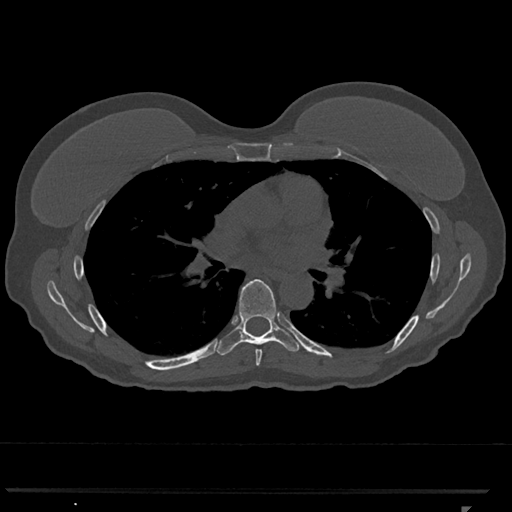
CT including the spine, one axial slice. Slice 725 of 793 in the series (ordered by position). Bone window (W 1800 / L 400 HU). 0.5 mm slice thickness. 512 × 512 image matrix, field of view 380 × 380 mm. Female patient, age 62 years. From the clinical record (not read from this slice): primary cancer: renal.
Outlined on this slice (semi-automatic segmentation, software-assisted and operator-edited):
- T6 vertebra: bounding box (x1, y1, x2, y2) in pixels: (255, 349, 262, 366)
- T7 vertebra: (215, 279, 302, 356)